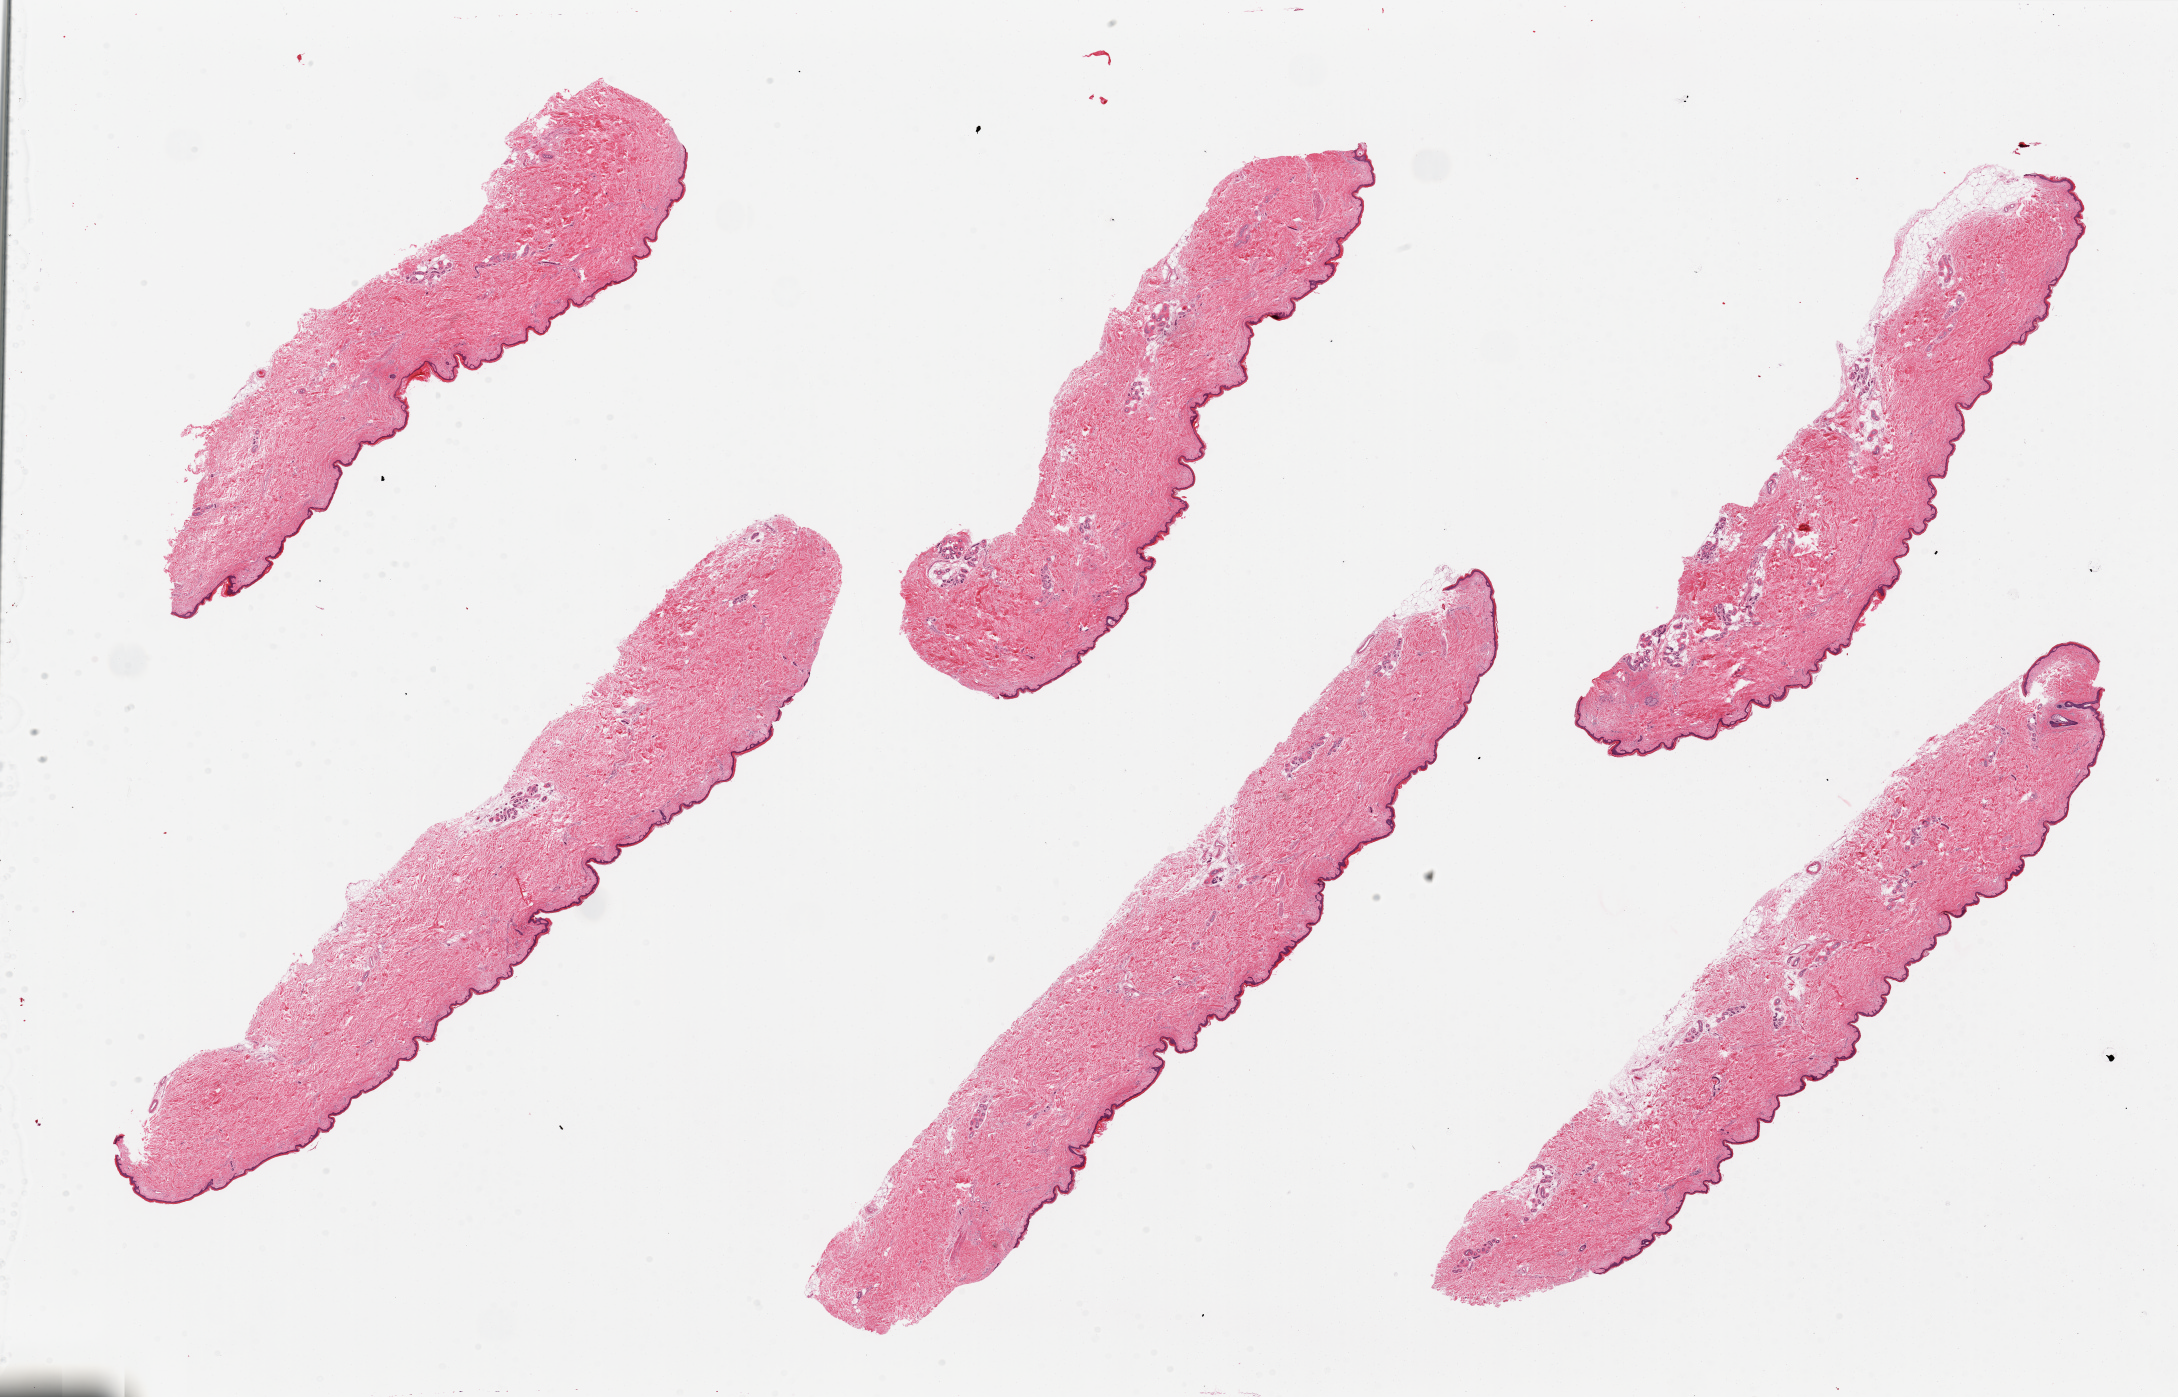
Digitized hematoxylin and eosin (H&E)-stained section, brightfield, shown as a low-resolution overview of the whole scanned area (about 34.5 x 22.1 mm, acquisition: 20x scan). PAXgene-fixed paraffin-embedded (PFPE) section. Sampled site (target tissue): skin of lower leg. Tissue donor sample. Donor: male.
- pathologist's review note for this sample: 6 pieces; well trimmed